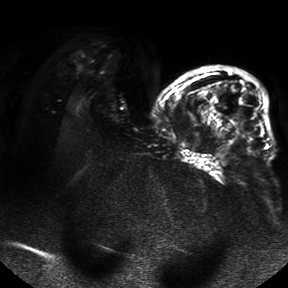
Breast MRI, one axial slice; slice 22 of 50 in the series (ordered by position); diffusion-weighted series; image 2 of 4 stored at this slice position (different b-values; order by instance number); 1.5 T; 4 mm slice thickness; 288 × 288 image matrix, field of view 390 × 390 mm. Female patient.
Structures marked on this image (manually delineated by an expert):
- tumour on diffusion-weighted imaging: box from (x=235, y=109) to (x=246, y=138) px